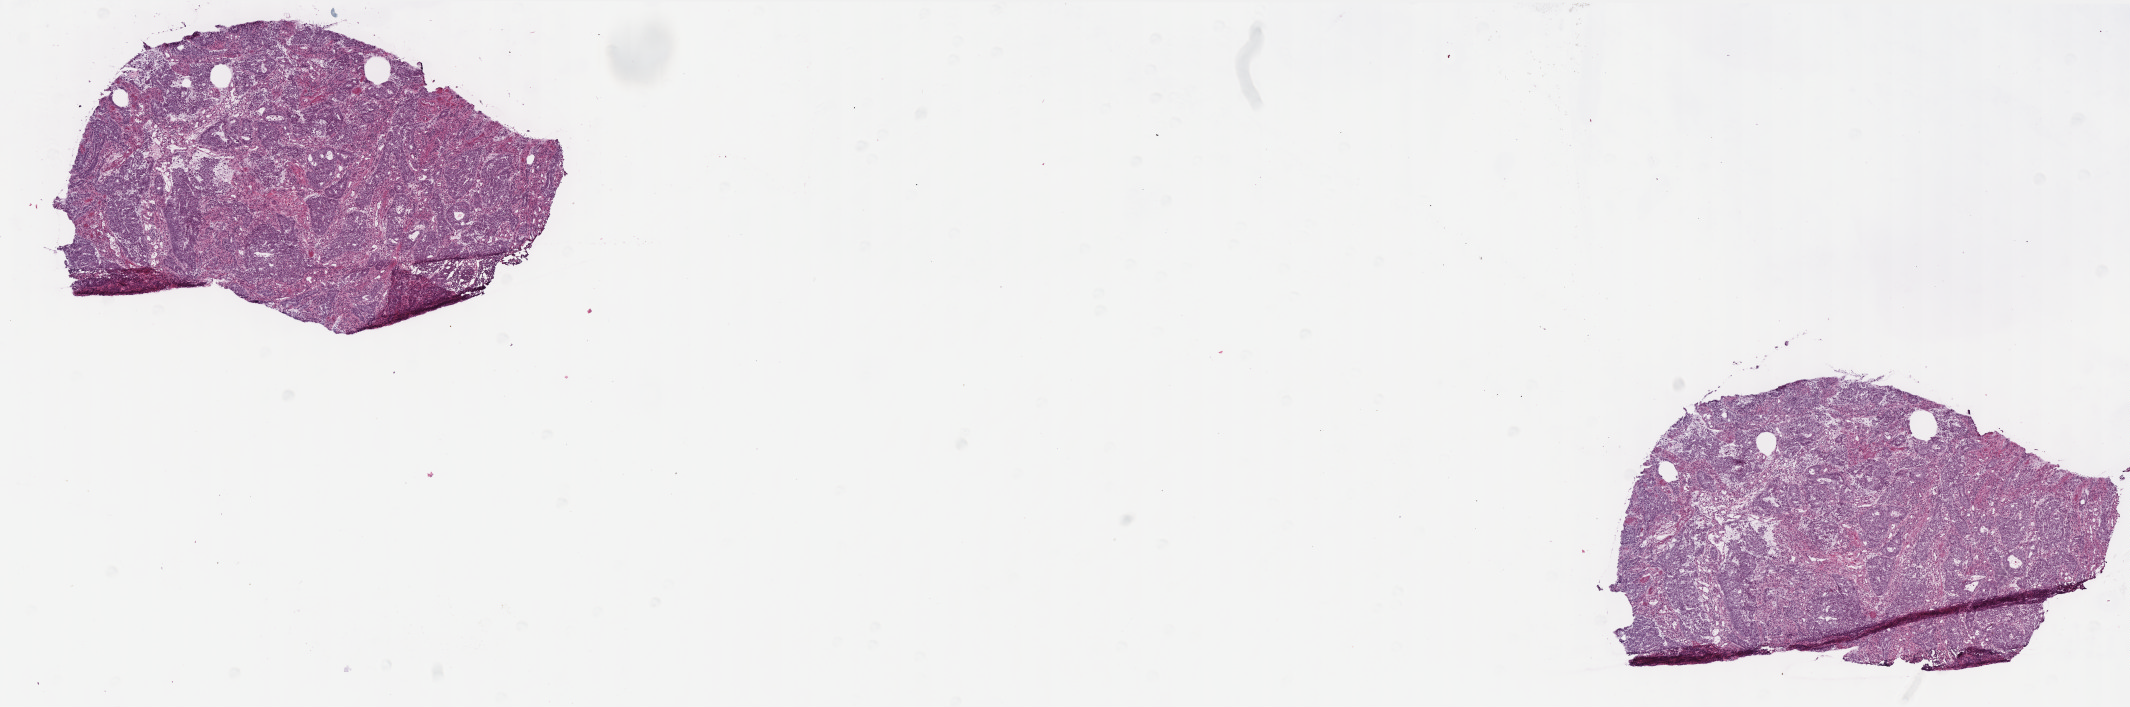
Digitized H&E tissue section (whole slide) — a low-resolution overview of the entire scanned area, about 17.1 x 5.7 mm. Frozen section. Colon, primary tumour sample. Male patient; age at initial diagnosis 50 years. Slide review estimates, as recorded: tumour cells 95%, tumour nuclei 80%, normal cells 0%, stromal cells 4%, necrosis 1%. Infiltration values recorded for this section: lymphocyte infiltration 13%, monocyte infiltration 1%, neutrophil infiltration 2%.
Pathologic diagnosis: Adenocarcinoma, NOS (ascending colon). AJCC pathologic stage: IIIB (6th edition).